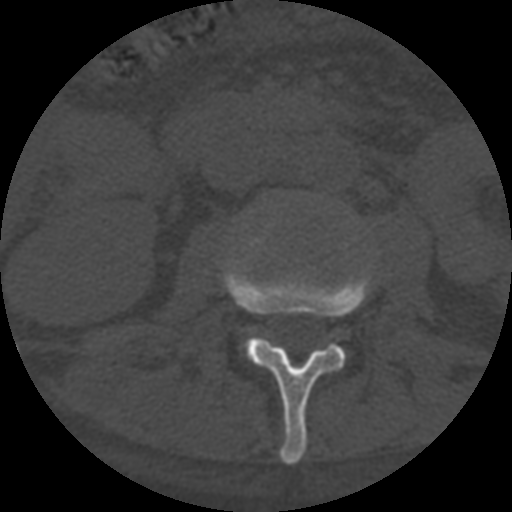
CT including the spine, one axial slice. Slice 252 of 708 in the series (ordered by position). Reconstruction kernel STANDARD. 120 kVp. One of 3 acquisitions stored at this slice position. Bone window (W 1800 / L 400 HU). 1.25 mm slice thickness. 512 × 512 image matrix, field of view 160 × 160 mm. Patient age 55 years. Case-level facts recorded for this patient, not image findings: primary cancer: colon.
Structures marked on this image (semi-automatic segmentation, software-assisted and operator-edited):
- L2 vertebra: bounding box (x1, y1, x2, y2) in pixels: (222, 222, 371, 465)